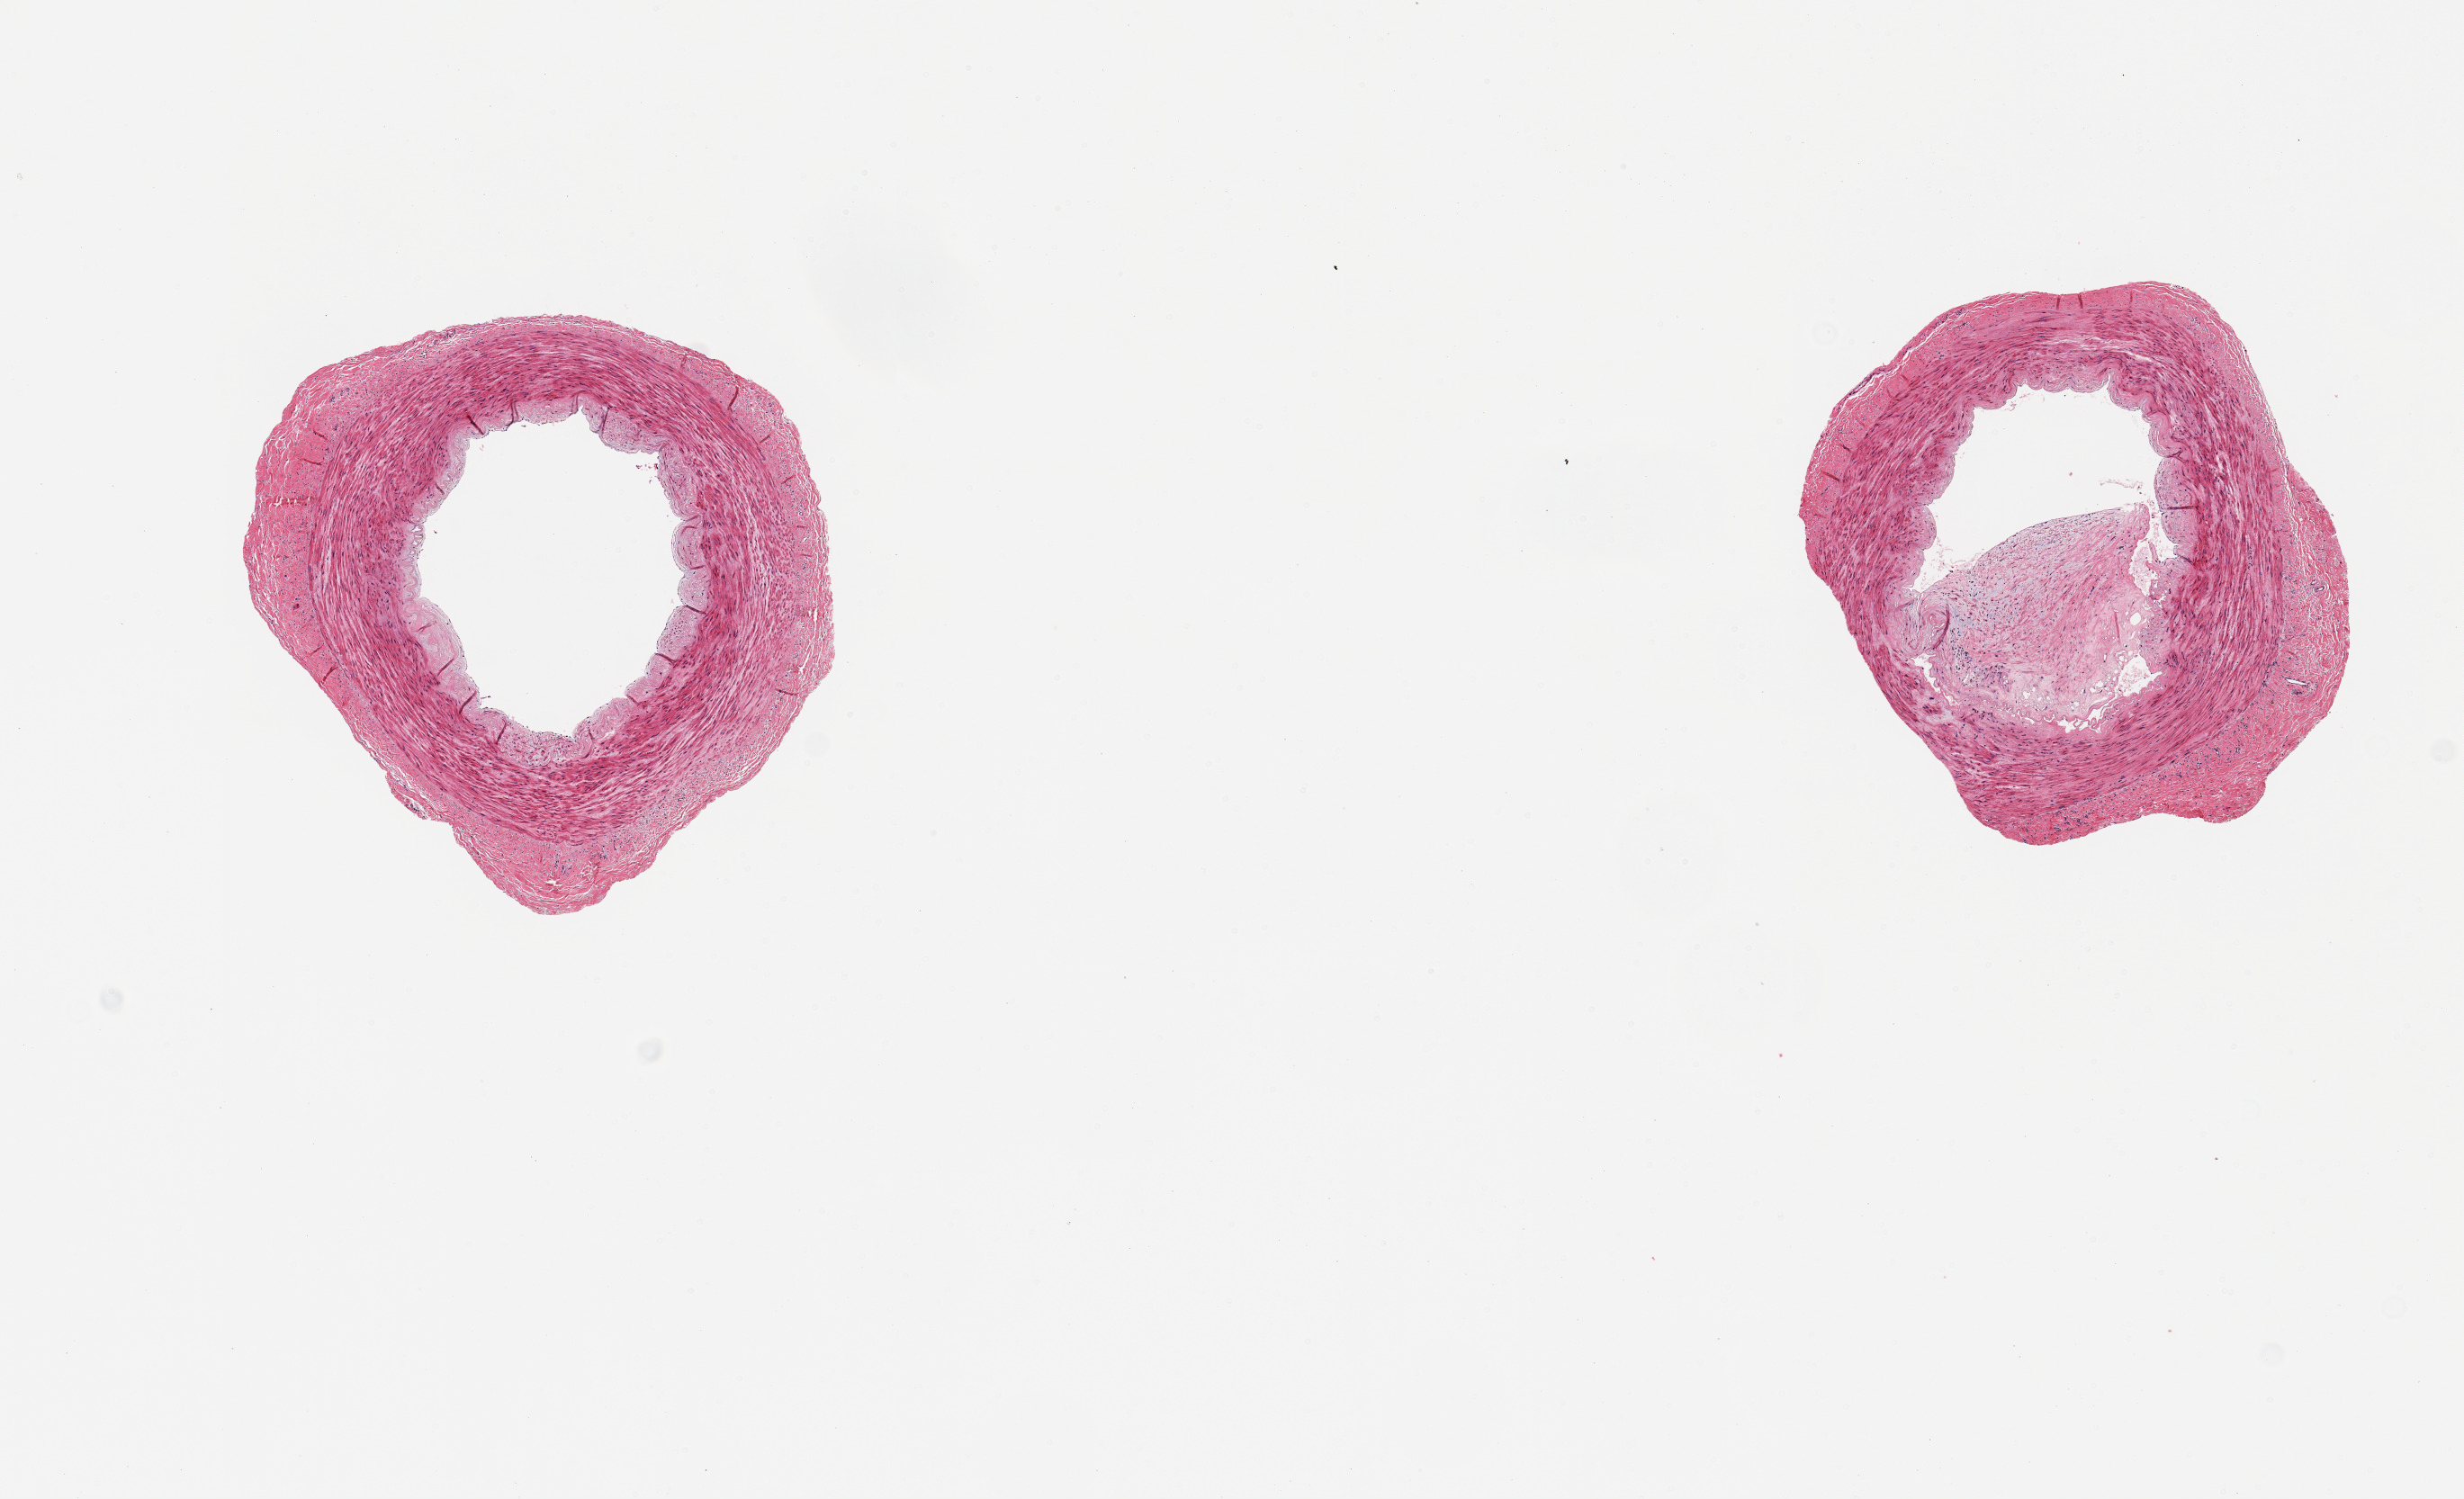
Haematoxylin and eosin whole-slide image, brightfield — a low-resolution overview of the entire scanned area, about 10.8 x 6.6 mm, PAXgene-fixed paraffin-embedded (PFPE) section, target tissue: tibial artery, tissue donor sample. Donor sex: male.
- pathologist's review note for this sample: 2 pieces, no adherent fat